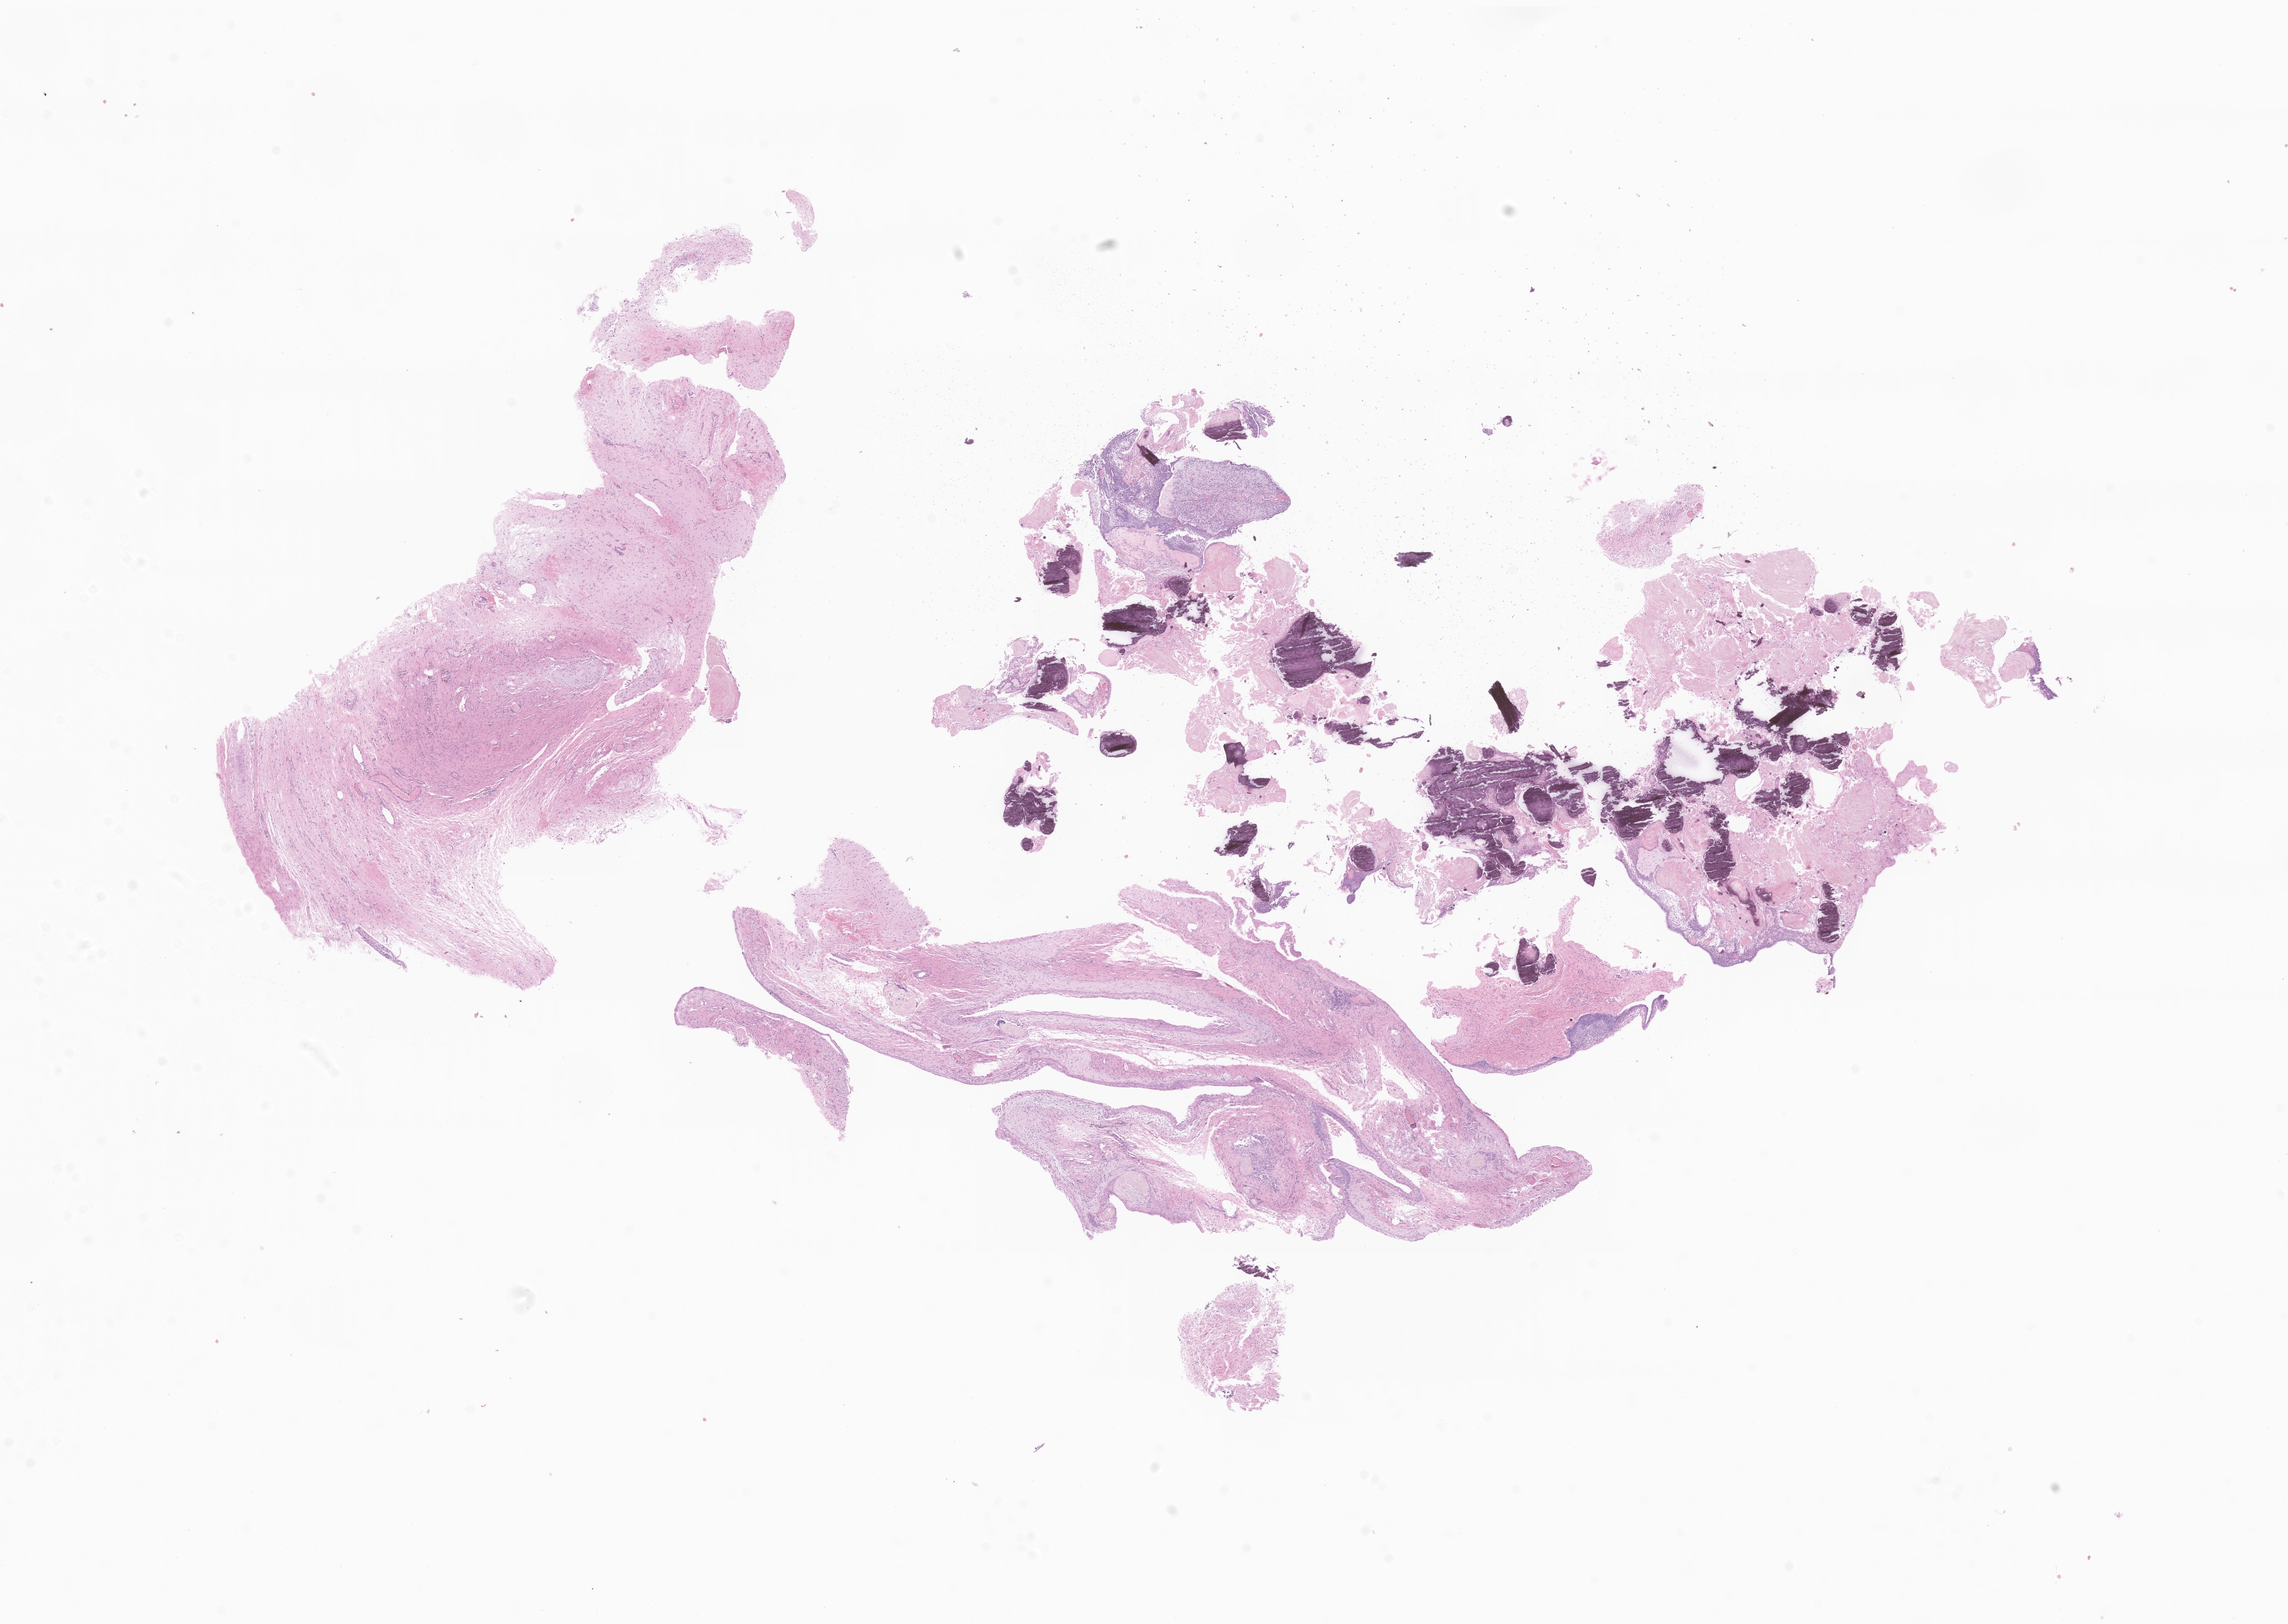
Digitized H&E-stained section of tumor tissue from the brain — shown as a low-resolution overview of the whole scanned area (about 19.4 x 13.8 mm); formalin-fixed, paraffin-embedded (FFPE) tissue. Patient: male, age 114 months.
Diagnosis (ICD-O-3 morphology term): Craniopharyngioma, adamantinomatous.